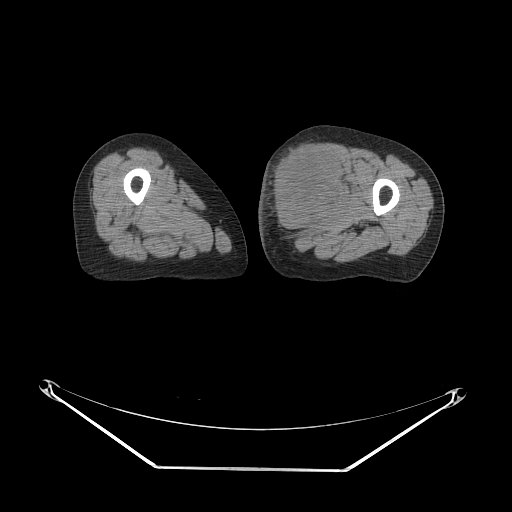
CT of an extremity soft-tissue mass (from a PET/CT study), one axial slice; position 38 of 91 along the scan axis; 140 kVp; soft-tissue window (W 400 / L 40 HU); 512 × 512 image matrix, field of view 500 × 500 mm. Female patient. Case-level facts recorded for this patient, not image findings: histological type: pleomorphic leiomyosarcoma; grade: high; site of the primary tumour: left thigh.
Annotated regions visible in this slice (expert contour drawn on MRI and transferred to this co-registered scan by the dataset authors):
- gross tumour volume including surrounding oedema: bounding box <269,141,350,238> (left, top, right, bottom; pixels)
- gross tumour volume (mass): <270,141,346,234>